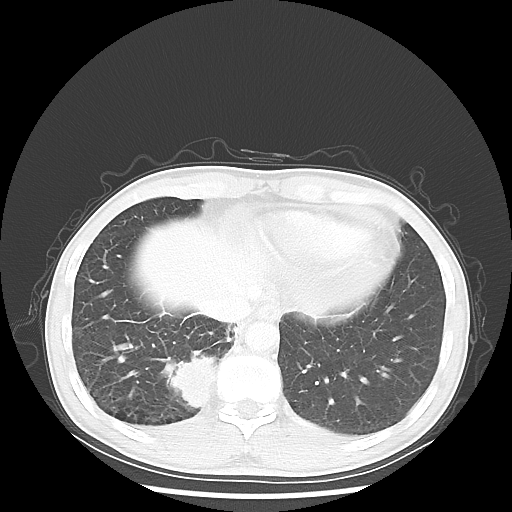
Chest CT, one axial slice; position 11 of 58 along the scan axis; reconstruction kernel LUNG; 100 kVp; lung window (W 1500 / L -600 HU); 5 mm slice thickness; 512 × 512 image matrix, field of view 360 × 360 mm. Patient: male, 56 years. From the clinical record (not read from this slice): clinical TNM (as recorded): T2 N1 M1; histopathological grade: G1.
Annotated regions visible in this slice (bounding box drawn by a radiologist):
- lung tumour (recorded histology: adenocarcinoma): box from (x=166, y=350) to (x=218, y=412) px